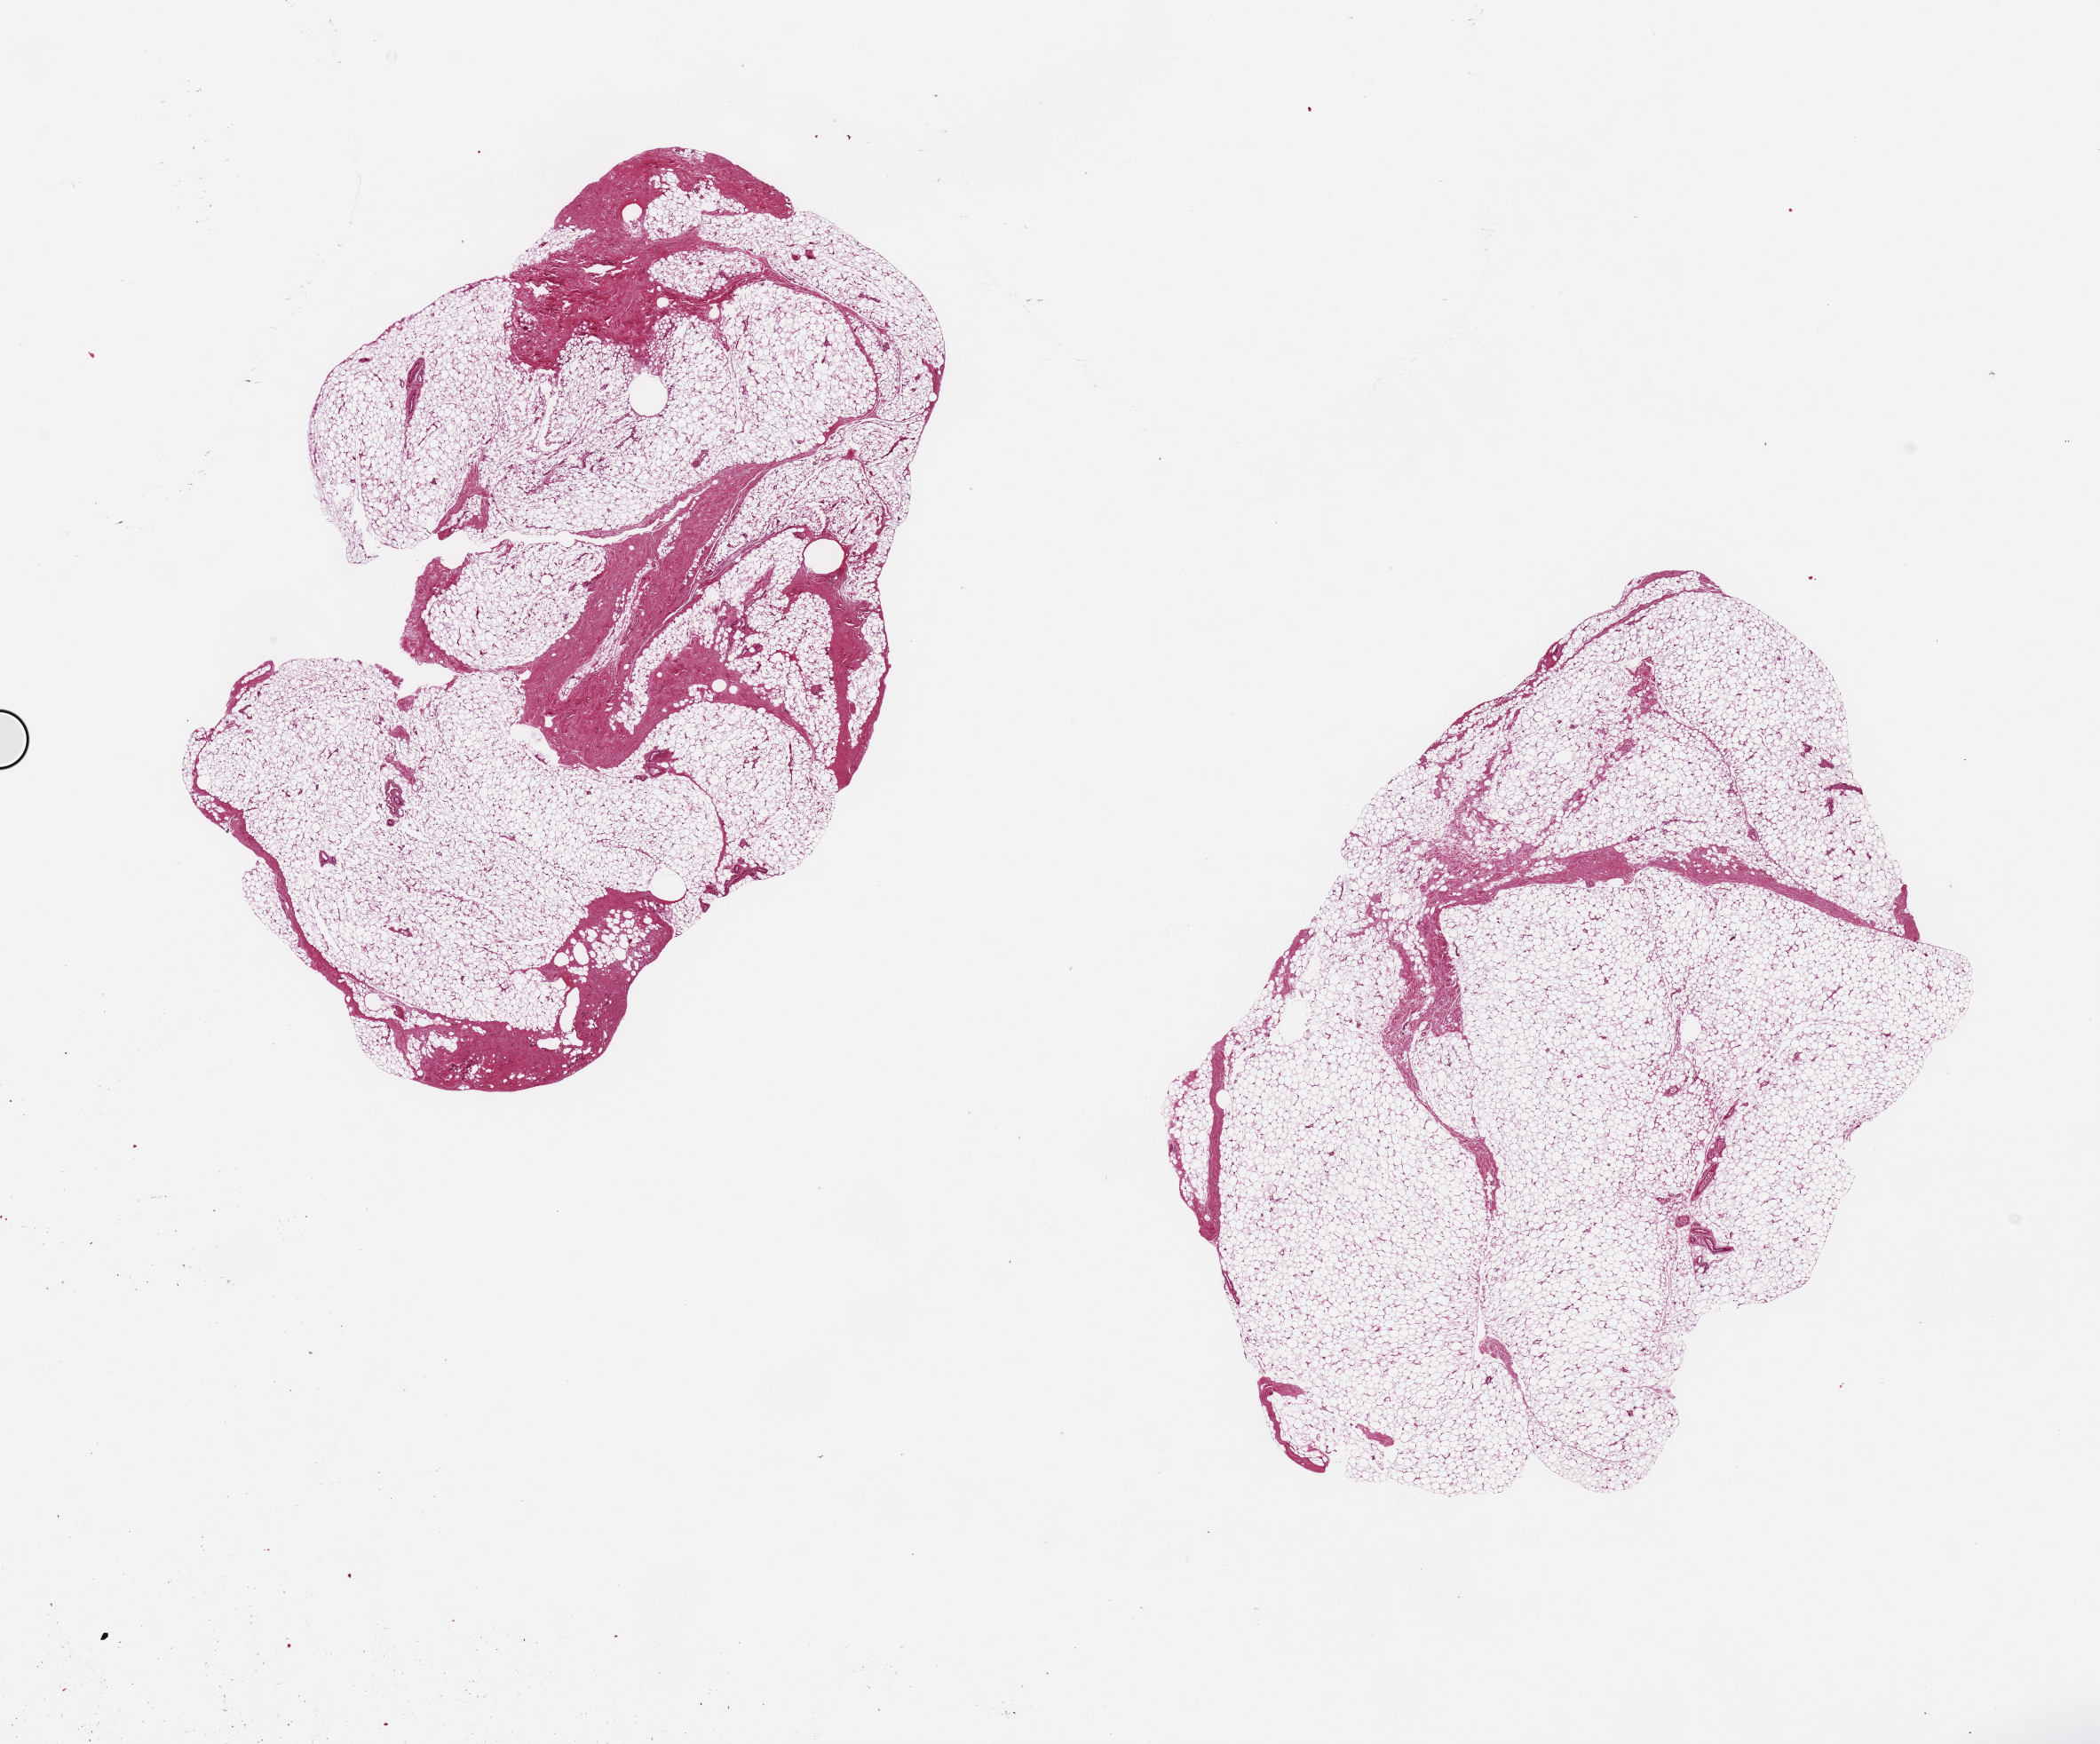
Digitized hematoxylin and eosin (H&E)-stained section, low-resolution overview of the scanned area, about 18.7 x 15.5 mm (acquisition: 20x scan); PAXgene-fixed paraffin-embedded (PFPE) section; target tissue: breast; donor tissue sample.
Pathologist's review note for this sample: 2 pieces, 9x7 & 9x6mm; all fibroadipose, no mammary ducts.